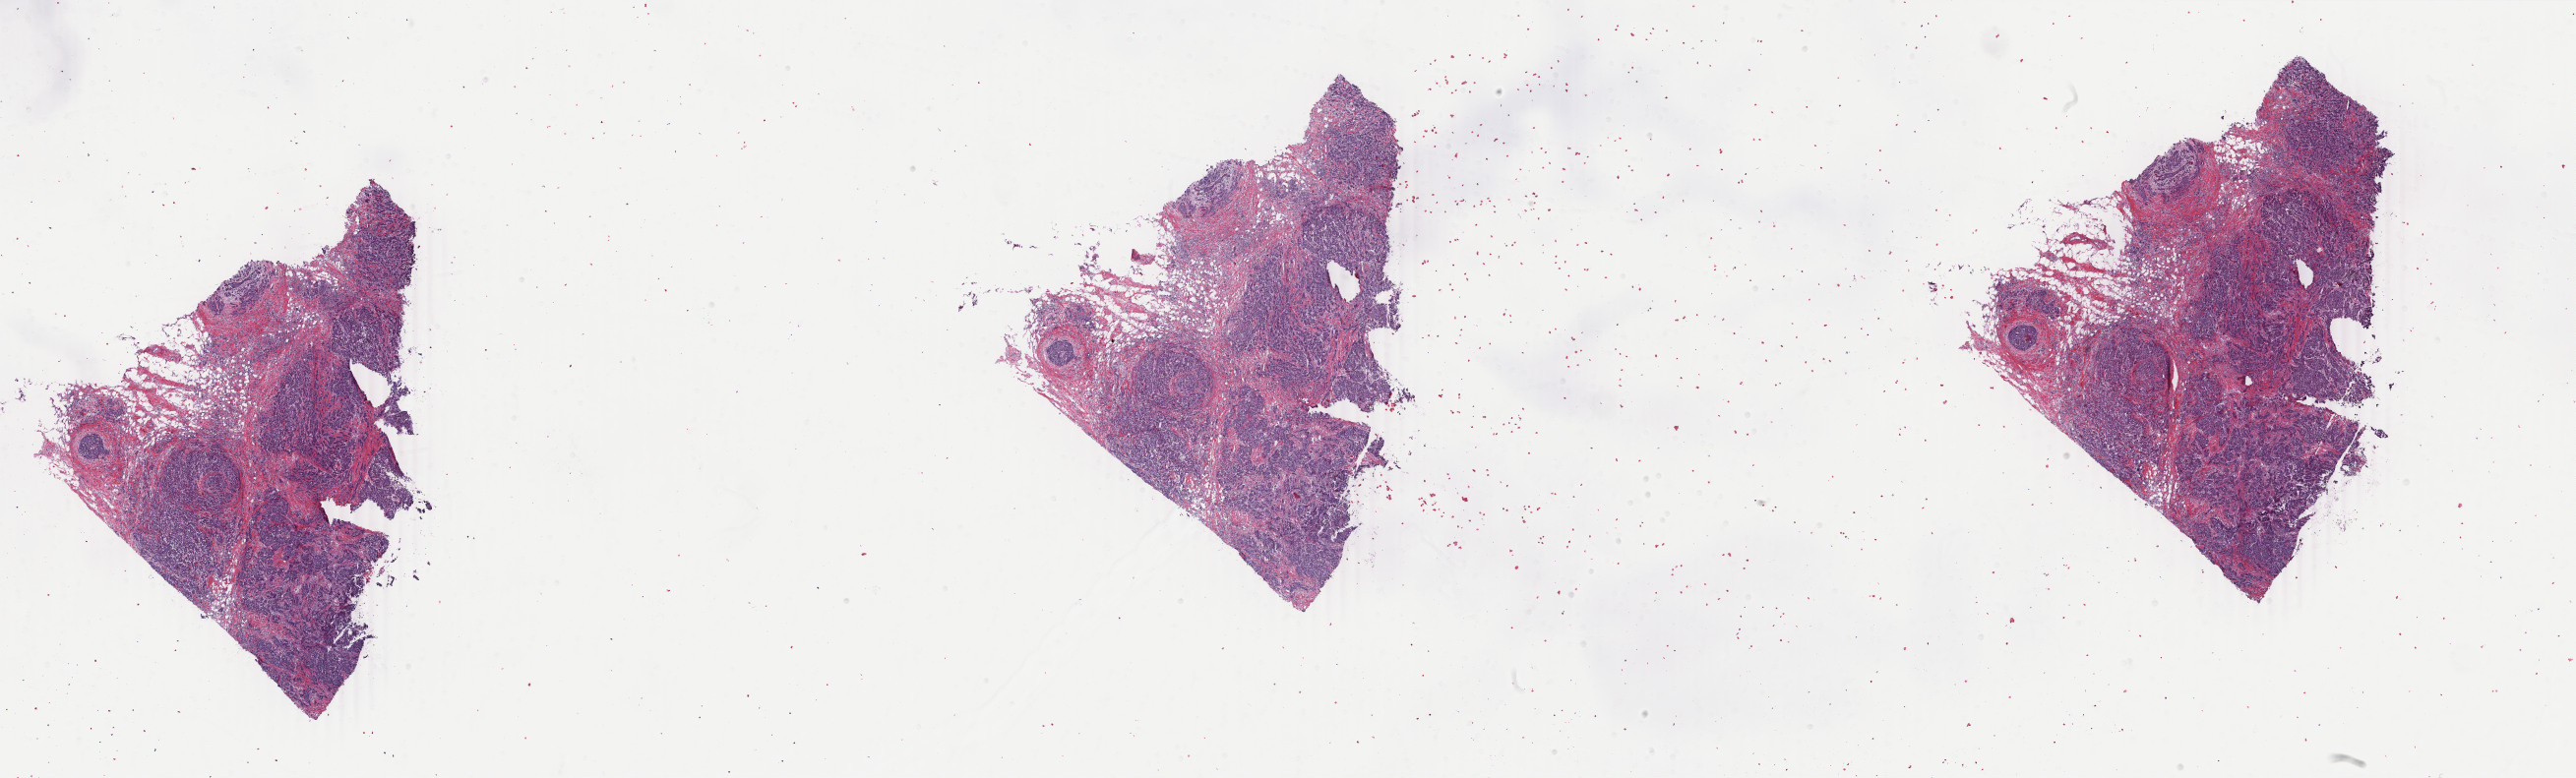
H&E-stained whole-slide image — low-resolution overview of the scanned area, about 41.6 x 12.6 mm (slide scanned at 40x). Frozen section from the top of the tissue portion. Primary tumour sample from the breast. Female patient; age at initial diagnosis 53 years. Pathologist review of this section (percent, as recorded): tumour cells 85%, tumour nuclei 85%, normal cells 2%, stromal cells 13%, necrosis 0%. Inflammatory infiltration, as recorded: lymphocyte infiltration 1%, monocyte infiltration 0%, neutrophil infiltration 0%.
• laterality: right
• AJCC pathologic stage: IIIA
• pathologic diagnosis: Infiltrating duct carcinoma, NOS
• lymph nodes positive (case pathology): 8 of 29 examined